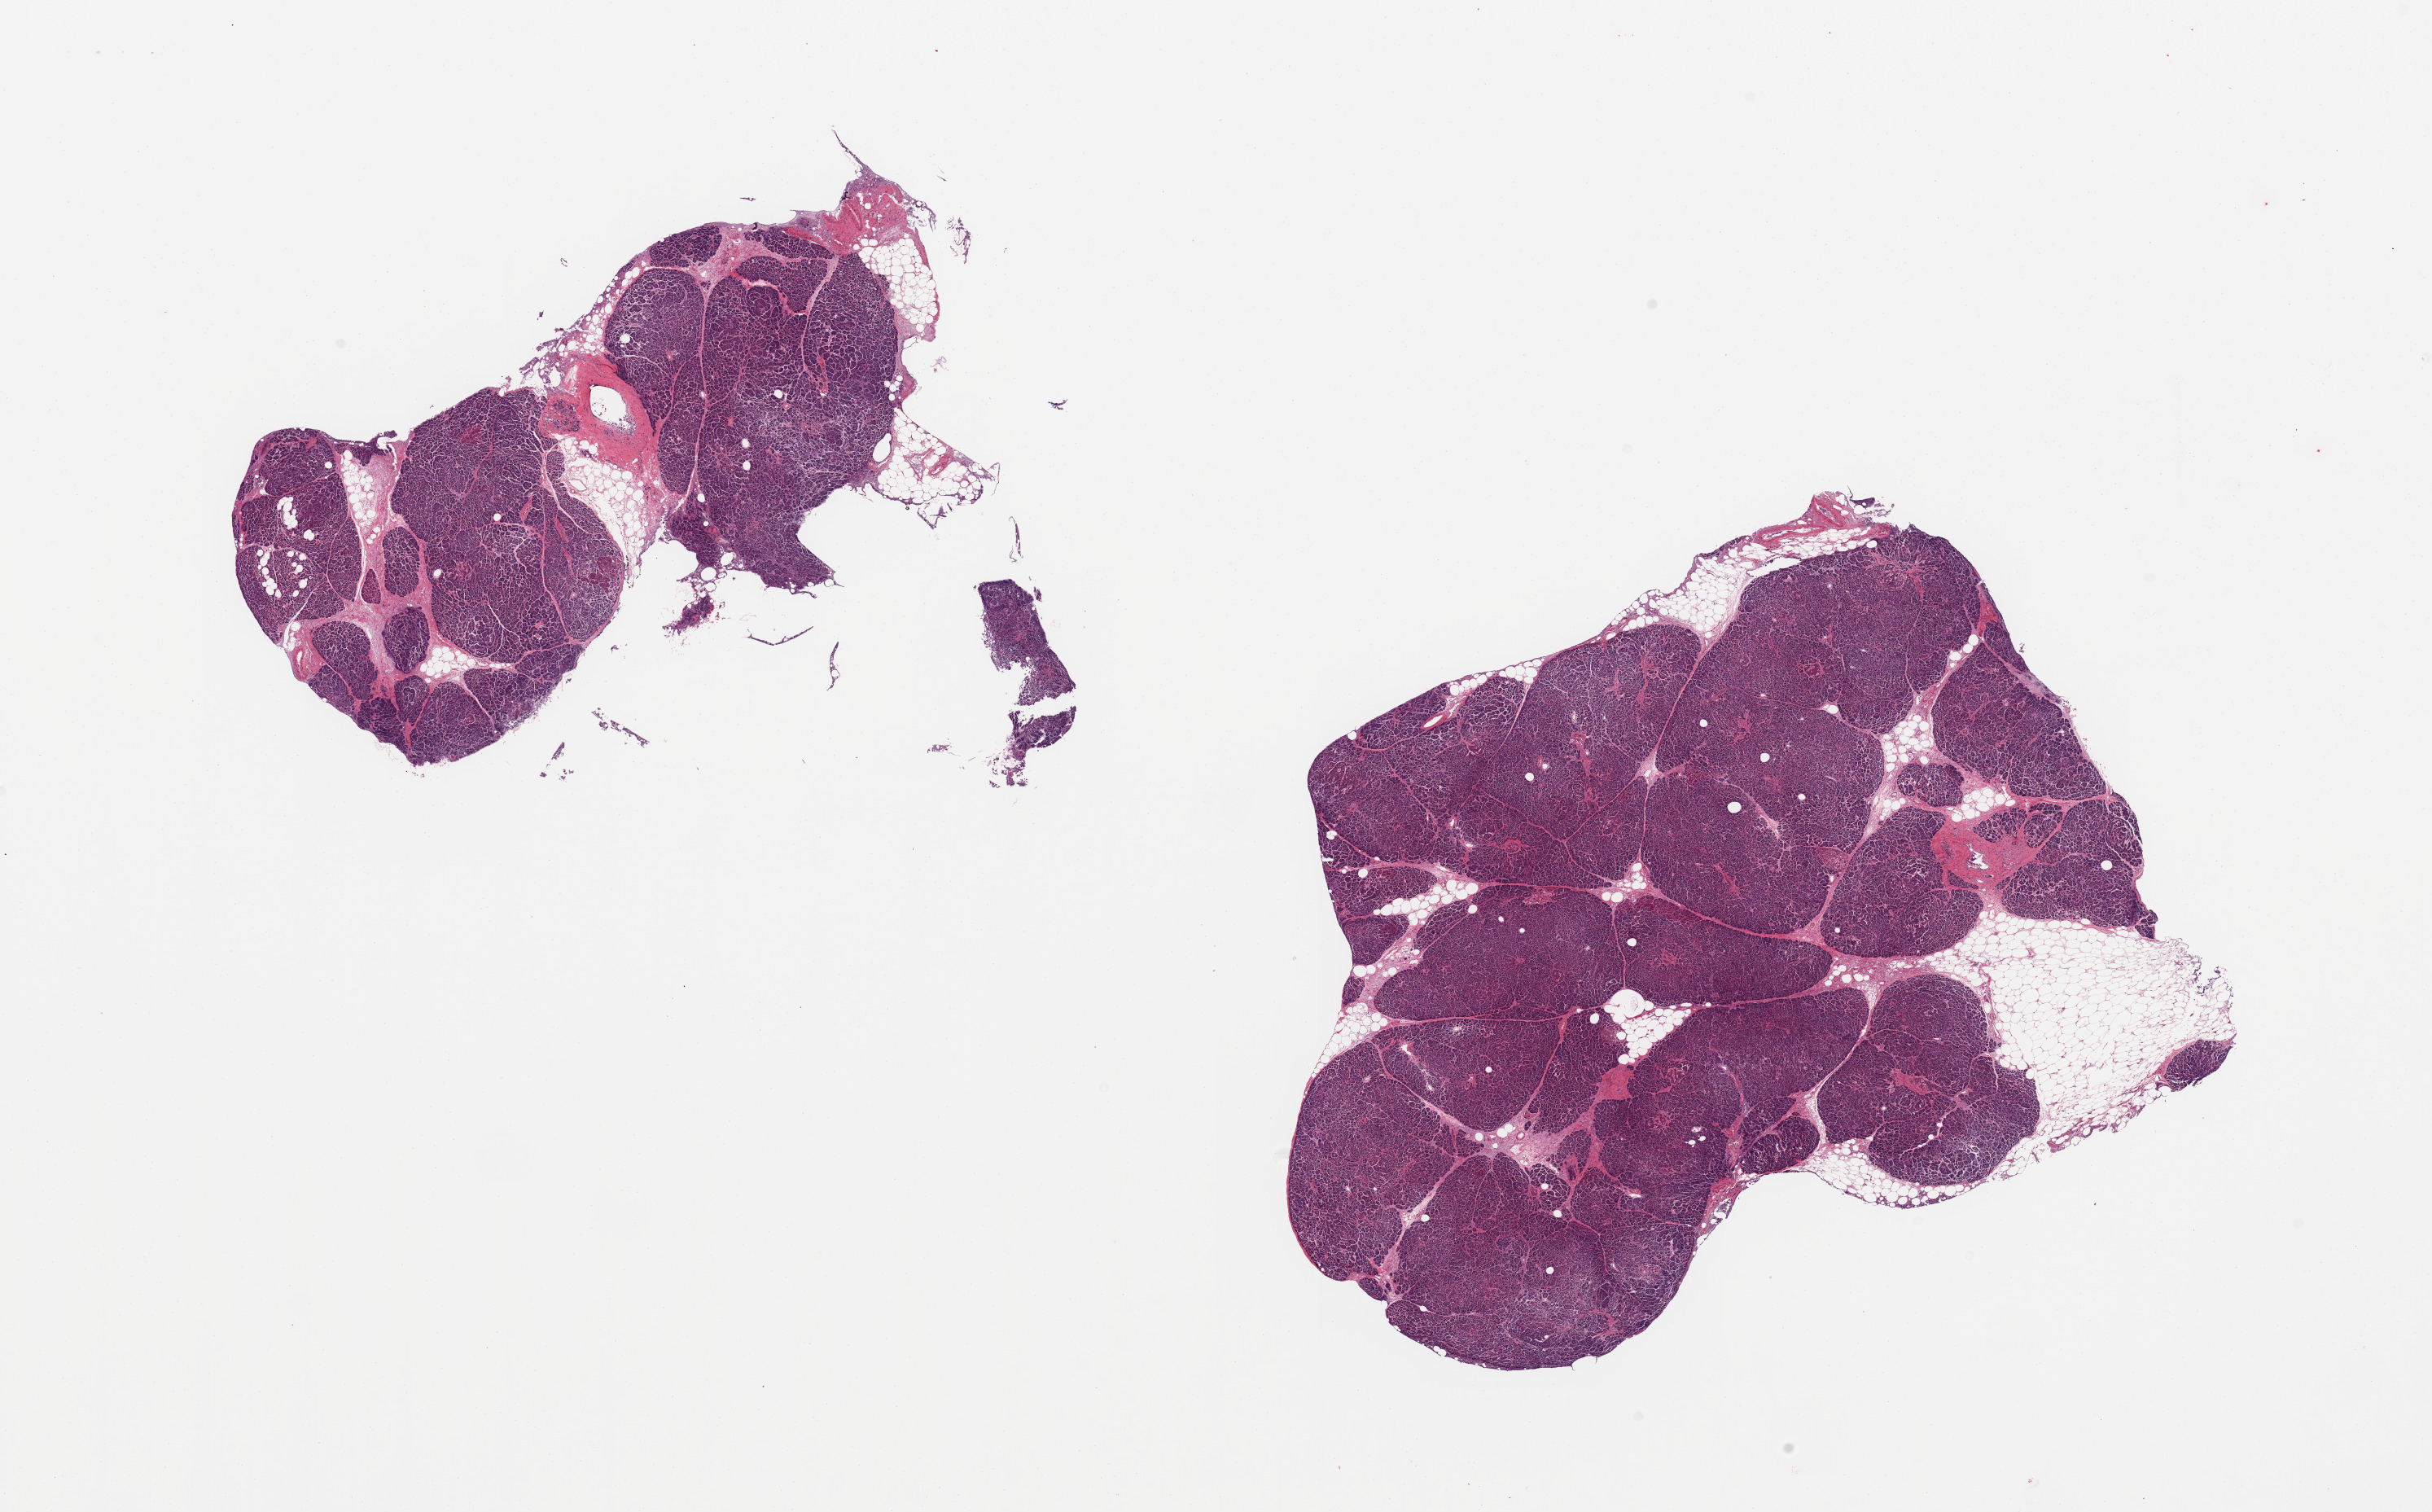
Whole-slide image, H&E stain — a low-resolution overview of the entire scanned area, about 23.6 x 14.7 mm (acquisition: 20x scan). PAXgene-fixed paraffin-embedded (PFPE) section. Sampled site (target tissue): pancreas. Donor tissue sample.
- pathologist's review note for this sample: 2 pieces, some areas centrally approach score '2'; islets still fairly well preserved and visible but not numerous. ~2mm nubbin of adherent fat